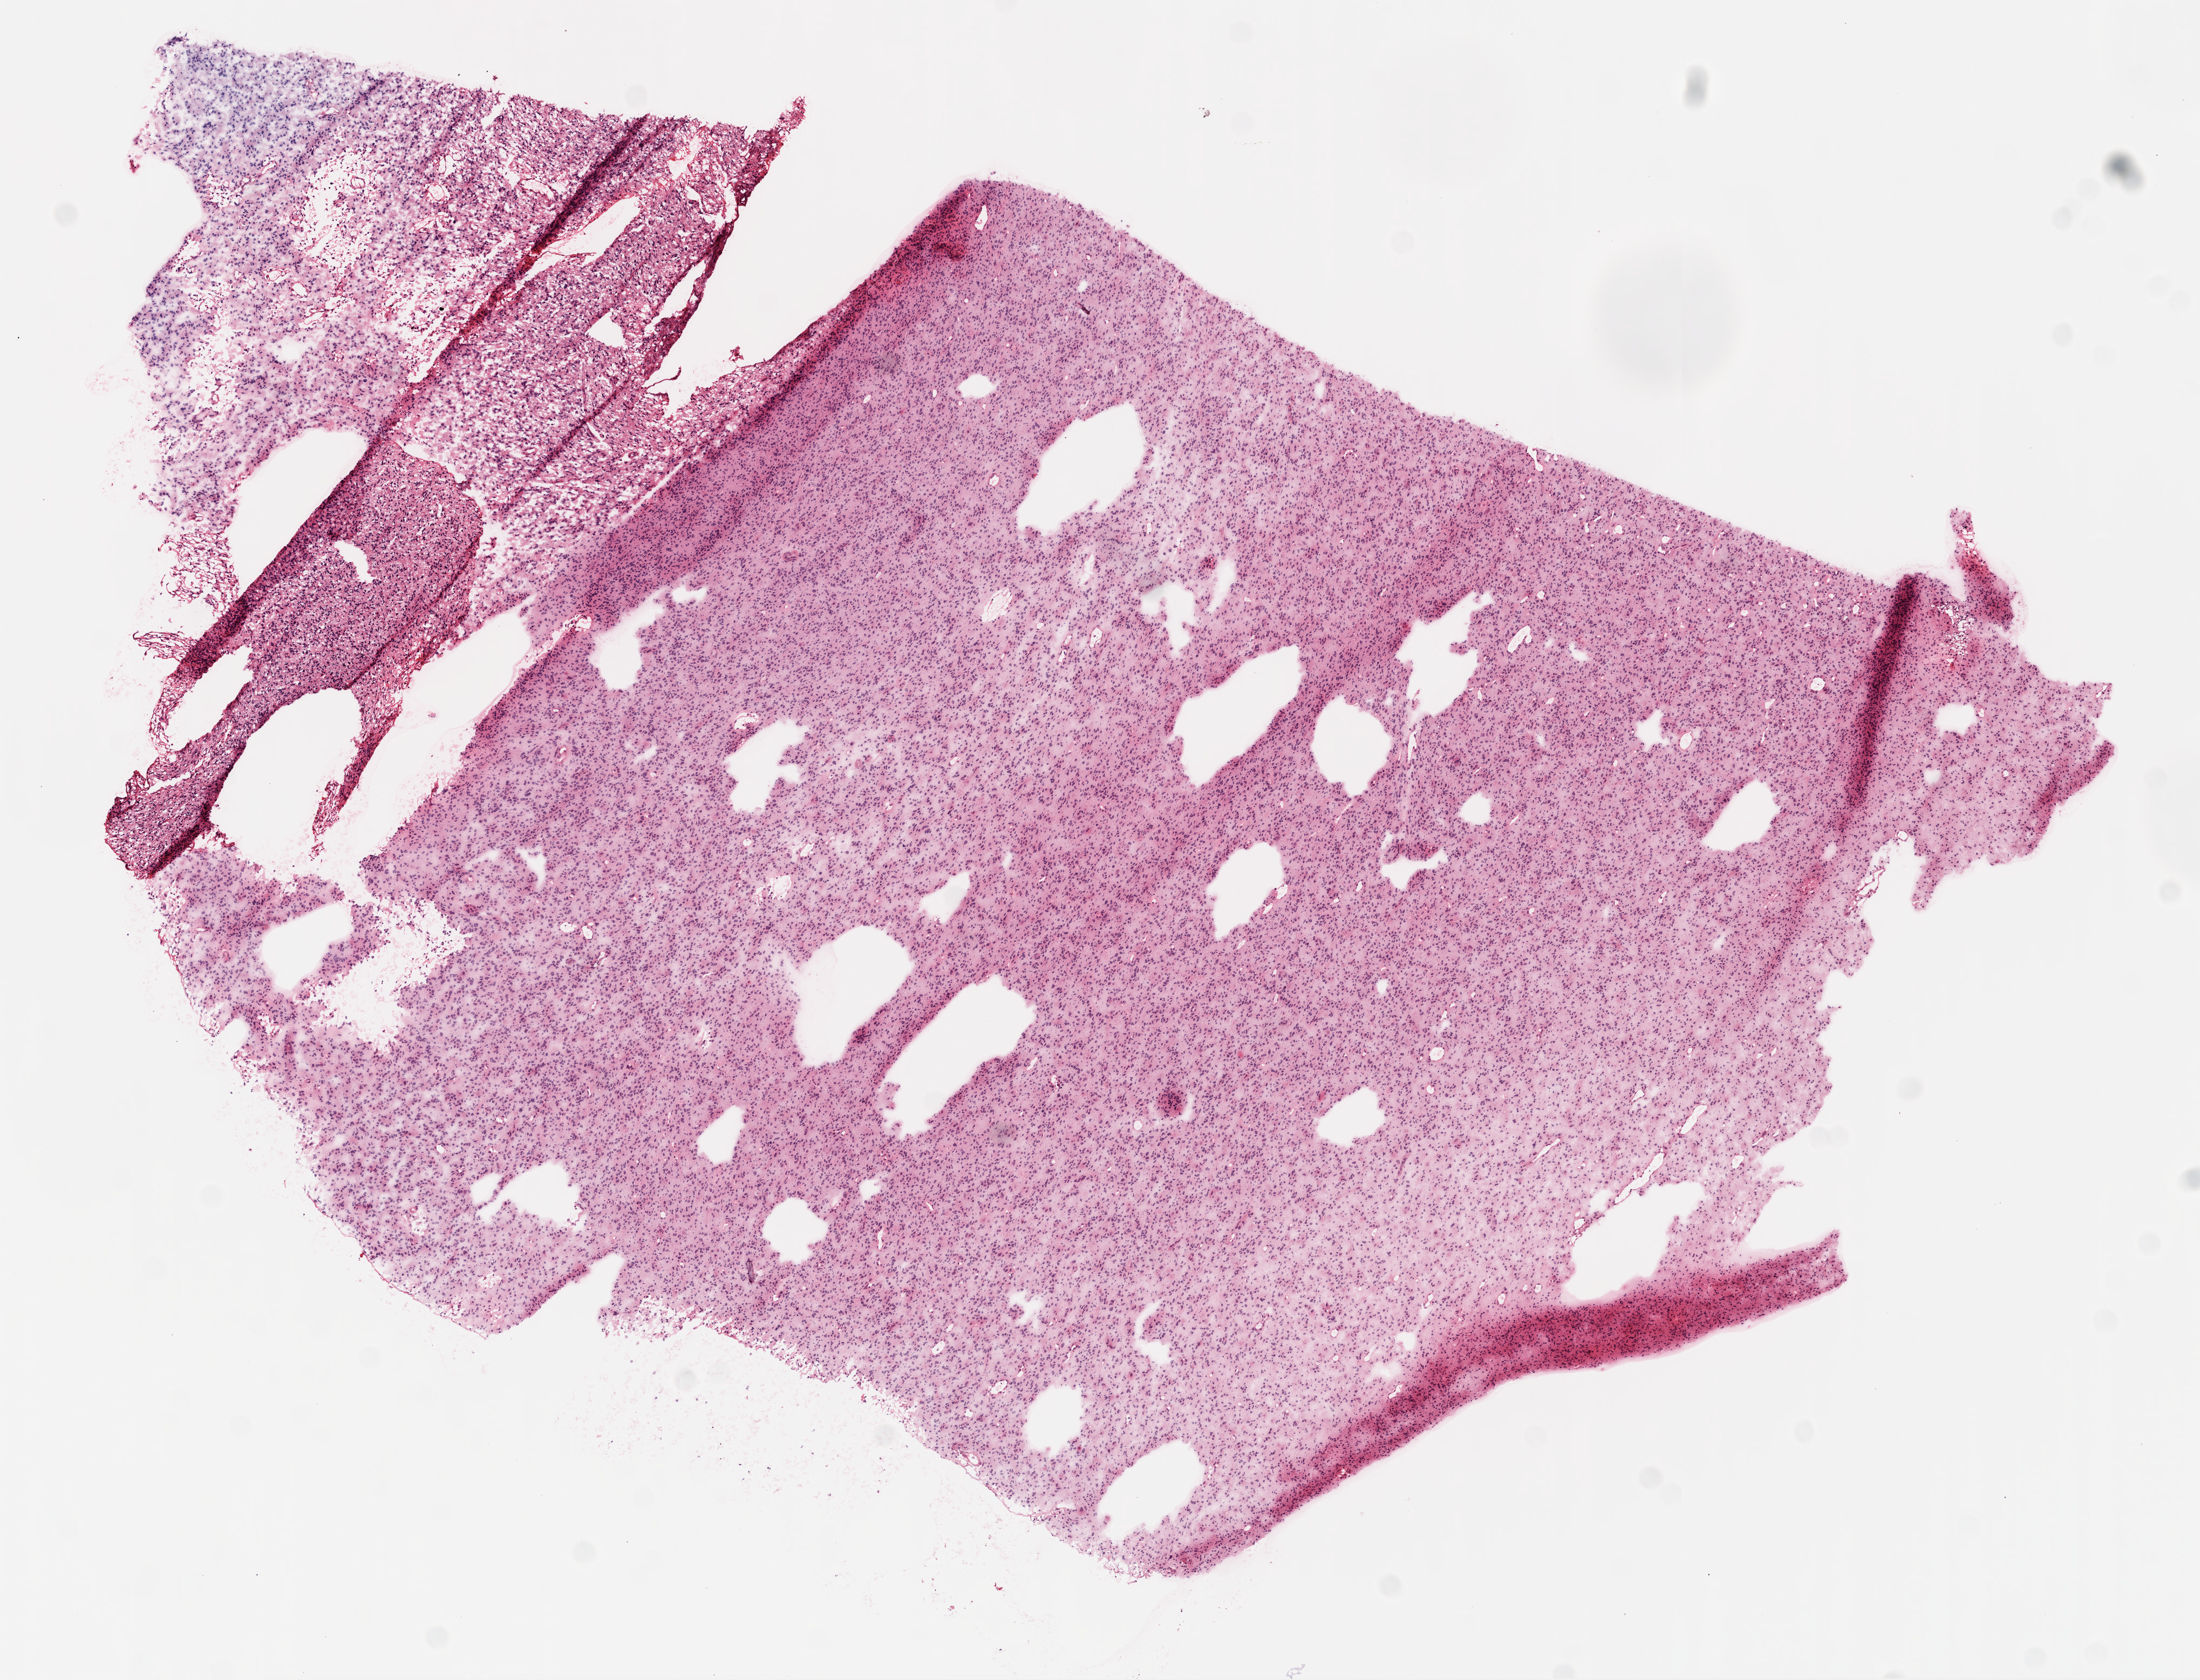
H&E whole-slide image — whole scanned area (about 8.2 x 6.3 mm) shown as a low-resolution overview. Frozen section from the top of the tissue portion. Sample: primary tumour, brain. Patient: female, age at initial diagnosis 30 years. Pathologist review of this section (percent, as recorded): tumour cells 80%, tumour nuclei 90%, normal cells 0%, stromal cells 10%, necrosis 10%.
• diagnosis: Glioblastoma